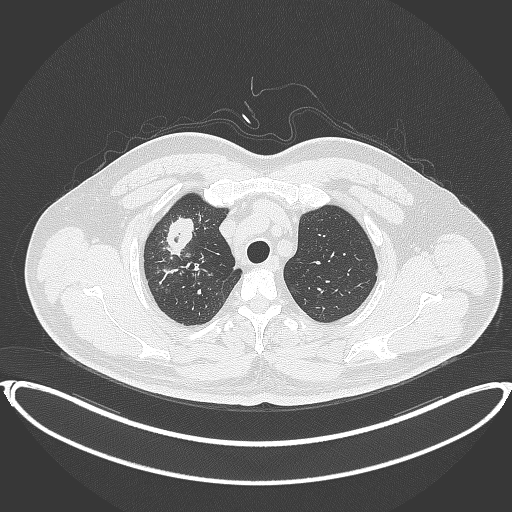
Chest CT, one axial slice; slice 323 of 399 in the series (ordered by position); reconstruction kernel B70f; lung window (W 1500 / L -600 HU); 1 mm slice thickness; 512 × 512 image matrix, field of view 445 × 445 mm. Male patient, age 53 years. Case-level facts recorded for this patient, not image findings: clinical TNM (as recorded): T2a N0 M0.
Outlined on this slice (rectangle marked by the reading radiologist):
- lung tumour (recorded histology: adenocarcinoma): bounding box [x1, y1, x2, y2] px = [165, 214, 195, 256]